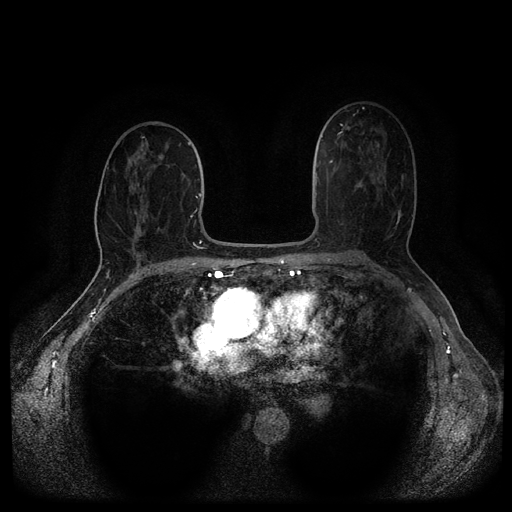
Breast MRI (dynamic contrast-enhanced, multi-phase), one axial slice. Slice 59 of 116 in the series (ordered by position). Dynamic contrast-enhanced series, time point 2 of 5 at this slice position (early post-contrast). 1.5 T. TE 2.6 ms, TR 5.4 ms. 2.1 mm slice thickness. 512 × 512 image matrix, field of view 340 × 340 mm. Female patient, age 69 years.
Annotated regions visible in this slice (semi-automatic segmentation, software-assisted and operator-edited):
- breast lesion (labelled benign in the annotation): bounding box [x1, y1, x2, y2] px = [373, 143, 380, 159]